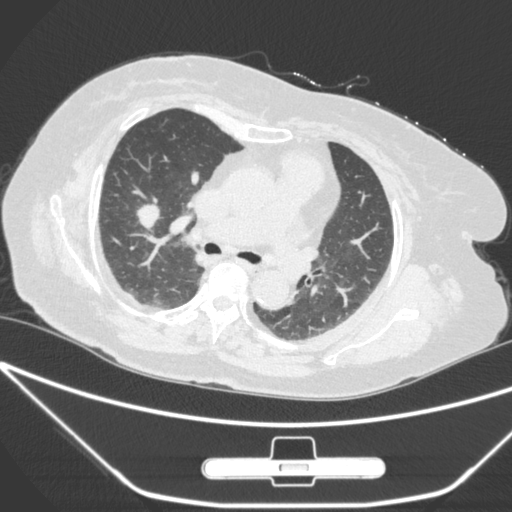
Chest CT, one axial slice. Position 162 of 245 along the scan axis. Lung window (W 1500 / L -600 HU). 1 mm slice thickness. 512 × 512 image matrix, field of view 365 × 365 mm. Patient: female, 65 years. From the clinical record (not read from this slice): clinical TNM (as recorded): T1c N0 M0; histopathological grade: G3.
Annotated regions visible in this slice (rectangle marked by the reading radiologist):
- lung tumour (recorded histology: adenocarcinoma): box from (x=134, y=196) to (x=162, y=238) px